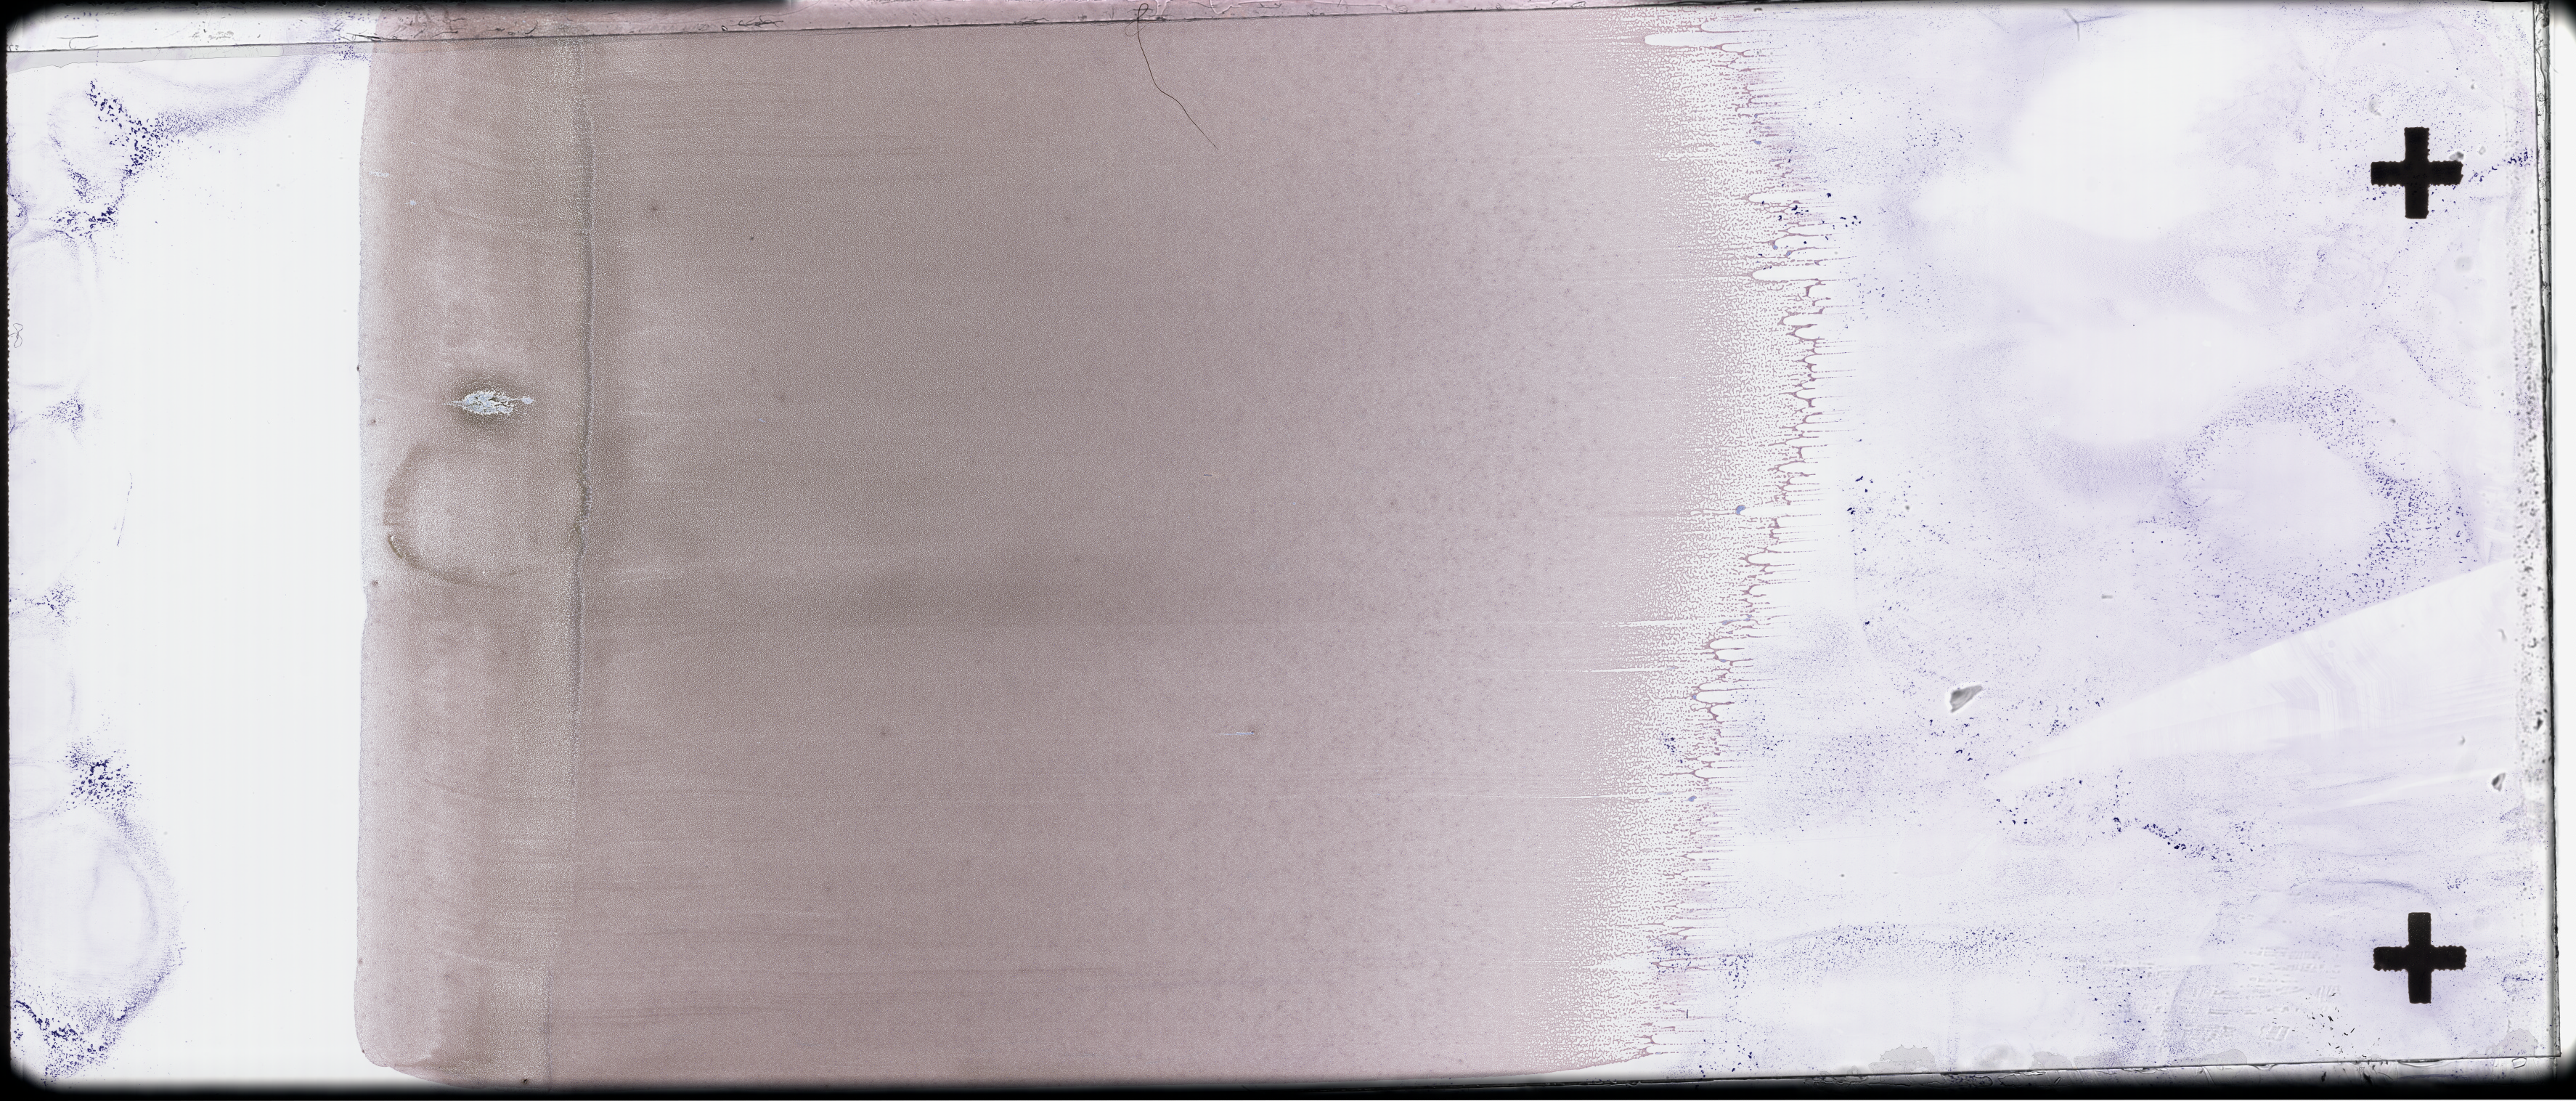
Wright–Giemsa-stained whole blood smear, whole-slide image, whole scanned area (about 57.3 x 24.5 mm) shown as a low-resolution overview, collected on treatment. Patient sex: male.
Patient diagnosis: Plasma Cell Myeloma.